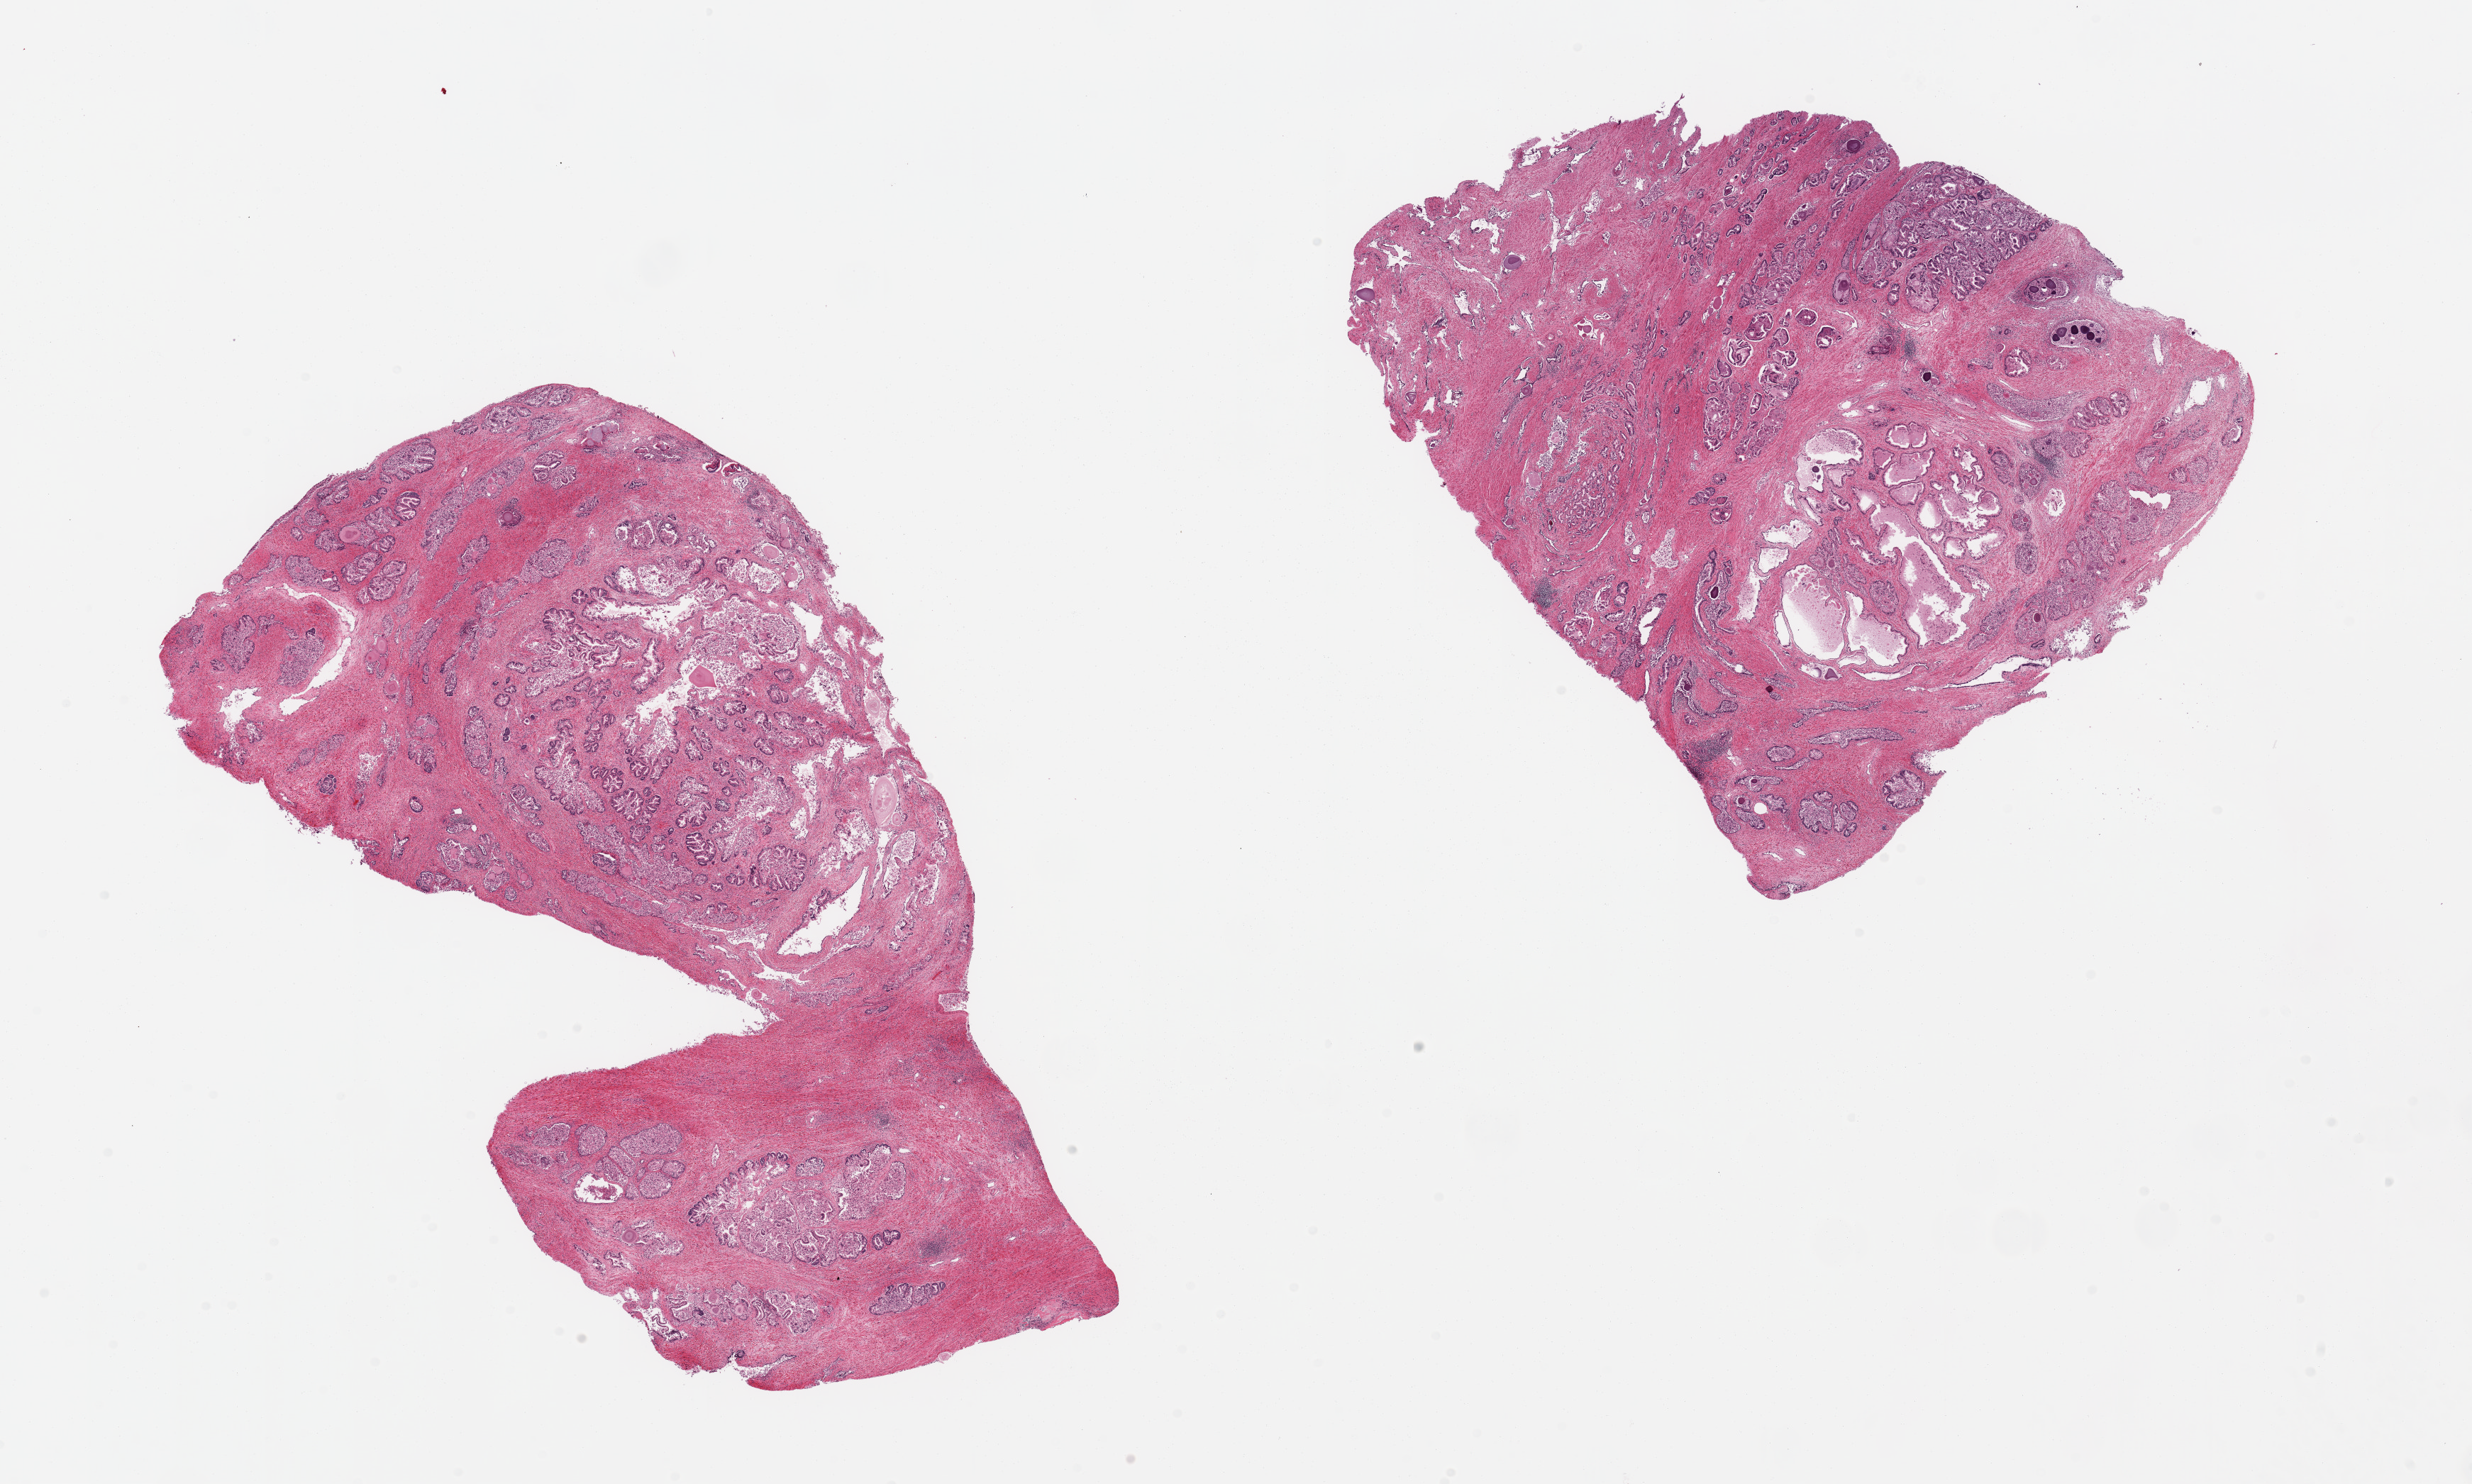
Haematoxylin and eosin whole-slide image, brightfield, a low-resolution overview of the entire scanned area, about 27.6 x 16.5 mm (slide scanned at 20x); PAXgene-fixed, paraffin-embedded tissue; section of prostate (target tissue); tissue donor sample. Donor: male.
Review note (as recorded): 2 pieces, nodular glandular/stromal hyperplasia, glandular elements moderately autolyzed.